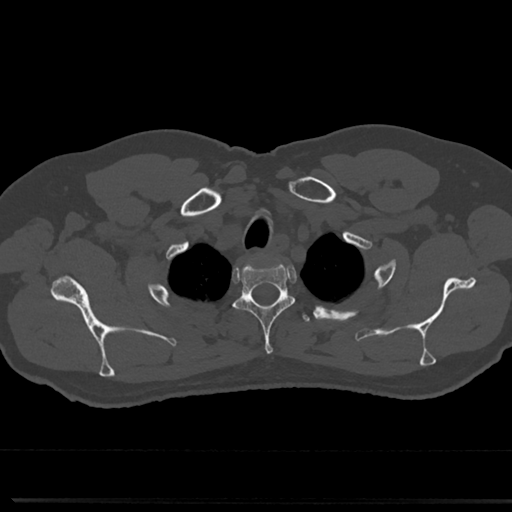
CT including the spine, one axial slice. Slice 632 of 817 in the series (ordered by position). Reconstruction kernel Br40s/3. 120 kVp. Bone window (W 1800 / L 400 HU). 0.5 mm slice thickness. 512 × 512 image matrix, field of view 355 × 355 mm. Patient: male, 61 years. Case-level facts recorded for this patient, not image findings: primary cancer: prostate.
Outlined on this slice (semi-automatic segmentation, software-assisted and operator-edited):
- T2 vertebra: bounding box (x1, y1, x2, y2) in pixels: (235, 254, 294, 356)
- T3 vertebra: (296, 312, 311, 326)